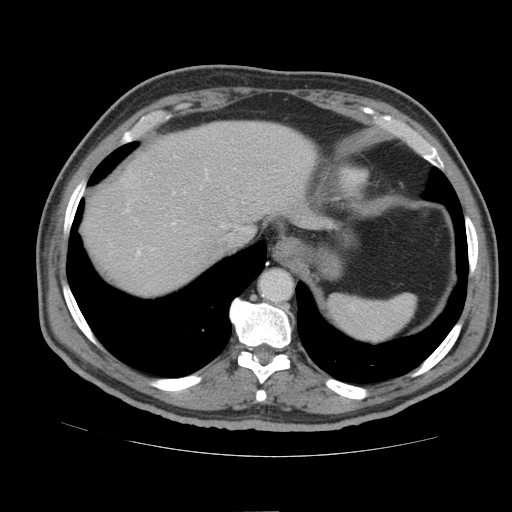
Contrast-enhanced abdominal CT (liver protocol), one axial slice; position 73 of 105 along the scan axis; 140 kVp; soft-tissue window (W 400 / L 40 HU); 2.5 mm slice thickness; 512 × 512 image matrix, field of view 380 × 380 mm. Case-level facts recorded for this patient, not image findings: diagnosis: hepatocellular carcinoma (patient treated with transarterial chemoembolisation; whether this scan precedes or follows treatment is not stated here); TNM stage (as recorded): Stage-IIIB; Child-Pugh class: A.
Structures marked on this image (semi-automatic segmentation, software-assisted and operator-edited):
- abdominal aorta: box from (x=261, y=270) to (x=292, y=300) px
- liver parenchyma outside the tumour (the mass and vessels are separate outlines, so this box may not span the whole liver): (x=82, y=120)–(x=332, y=294)
- liver vessels: (x=137, y=223)–(x=174, y=255)